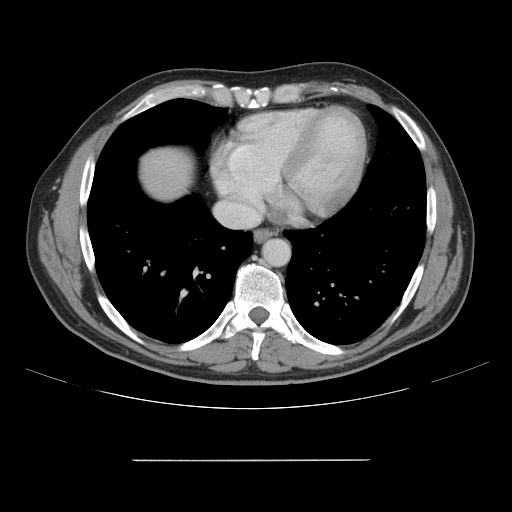
Contrast-enhanced abdominal CT, one axial slice; slice 150 of 164 in the series (ordered by position); 120 kVp; intravenous contrast given; soft-tissue window (W 400 / L 40 HU); 2.5 mm slice thickness; 512 × 512 image matrix, field of view 404 × 404 mm. Male patient, age 54 years. Case-level facts recorded for this patient, not image findings: diagnosis: colorectal cancer liver metastases, imaged before liver resection; multiple liver metastases: yes; largest metastasis: 1 cm.
Structures marked on this image (outlined manually by an expert reader):
- hepatic veins: bounding box <216,202,258,226> (left, top, right, bottom; pixels)
- liver: <139,150,192,198>
- planned liver remnant (the part of the liver to remain after resection): <139,150,191,198>